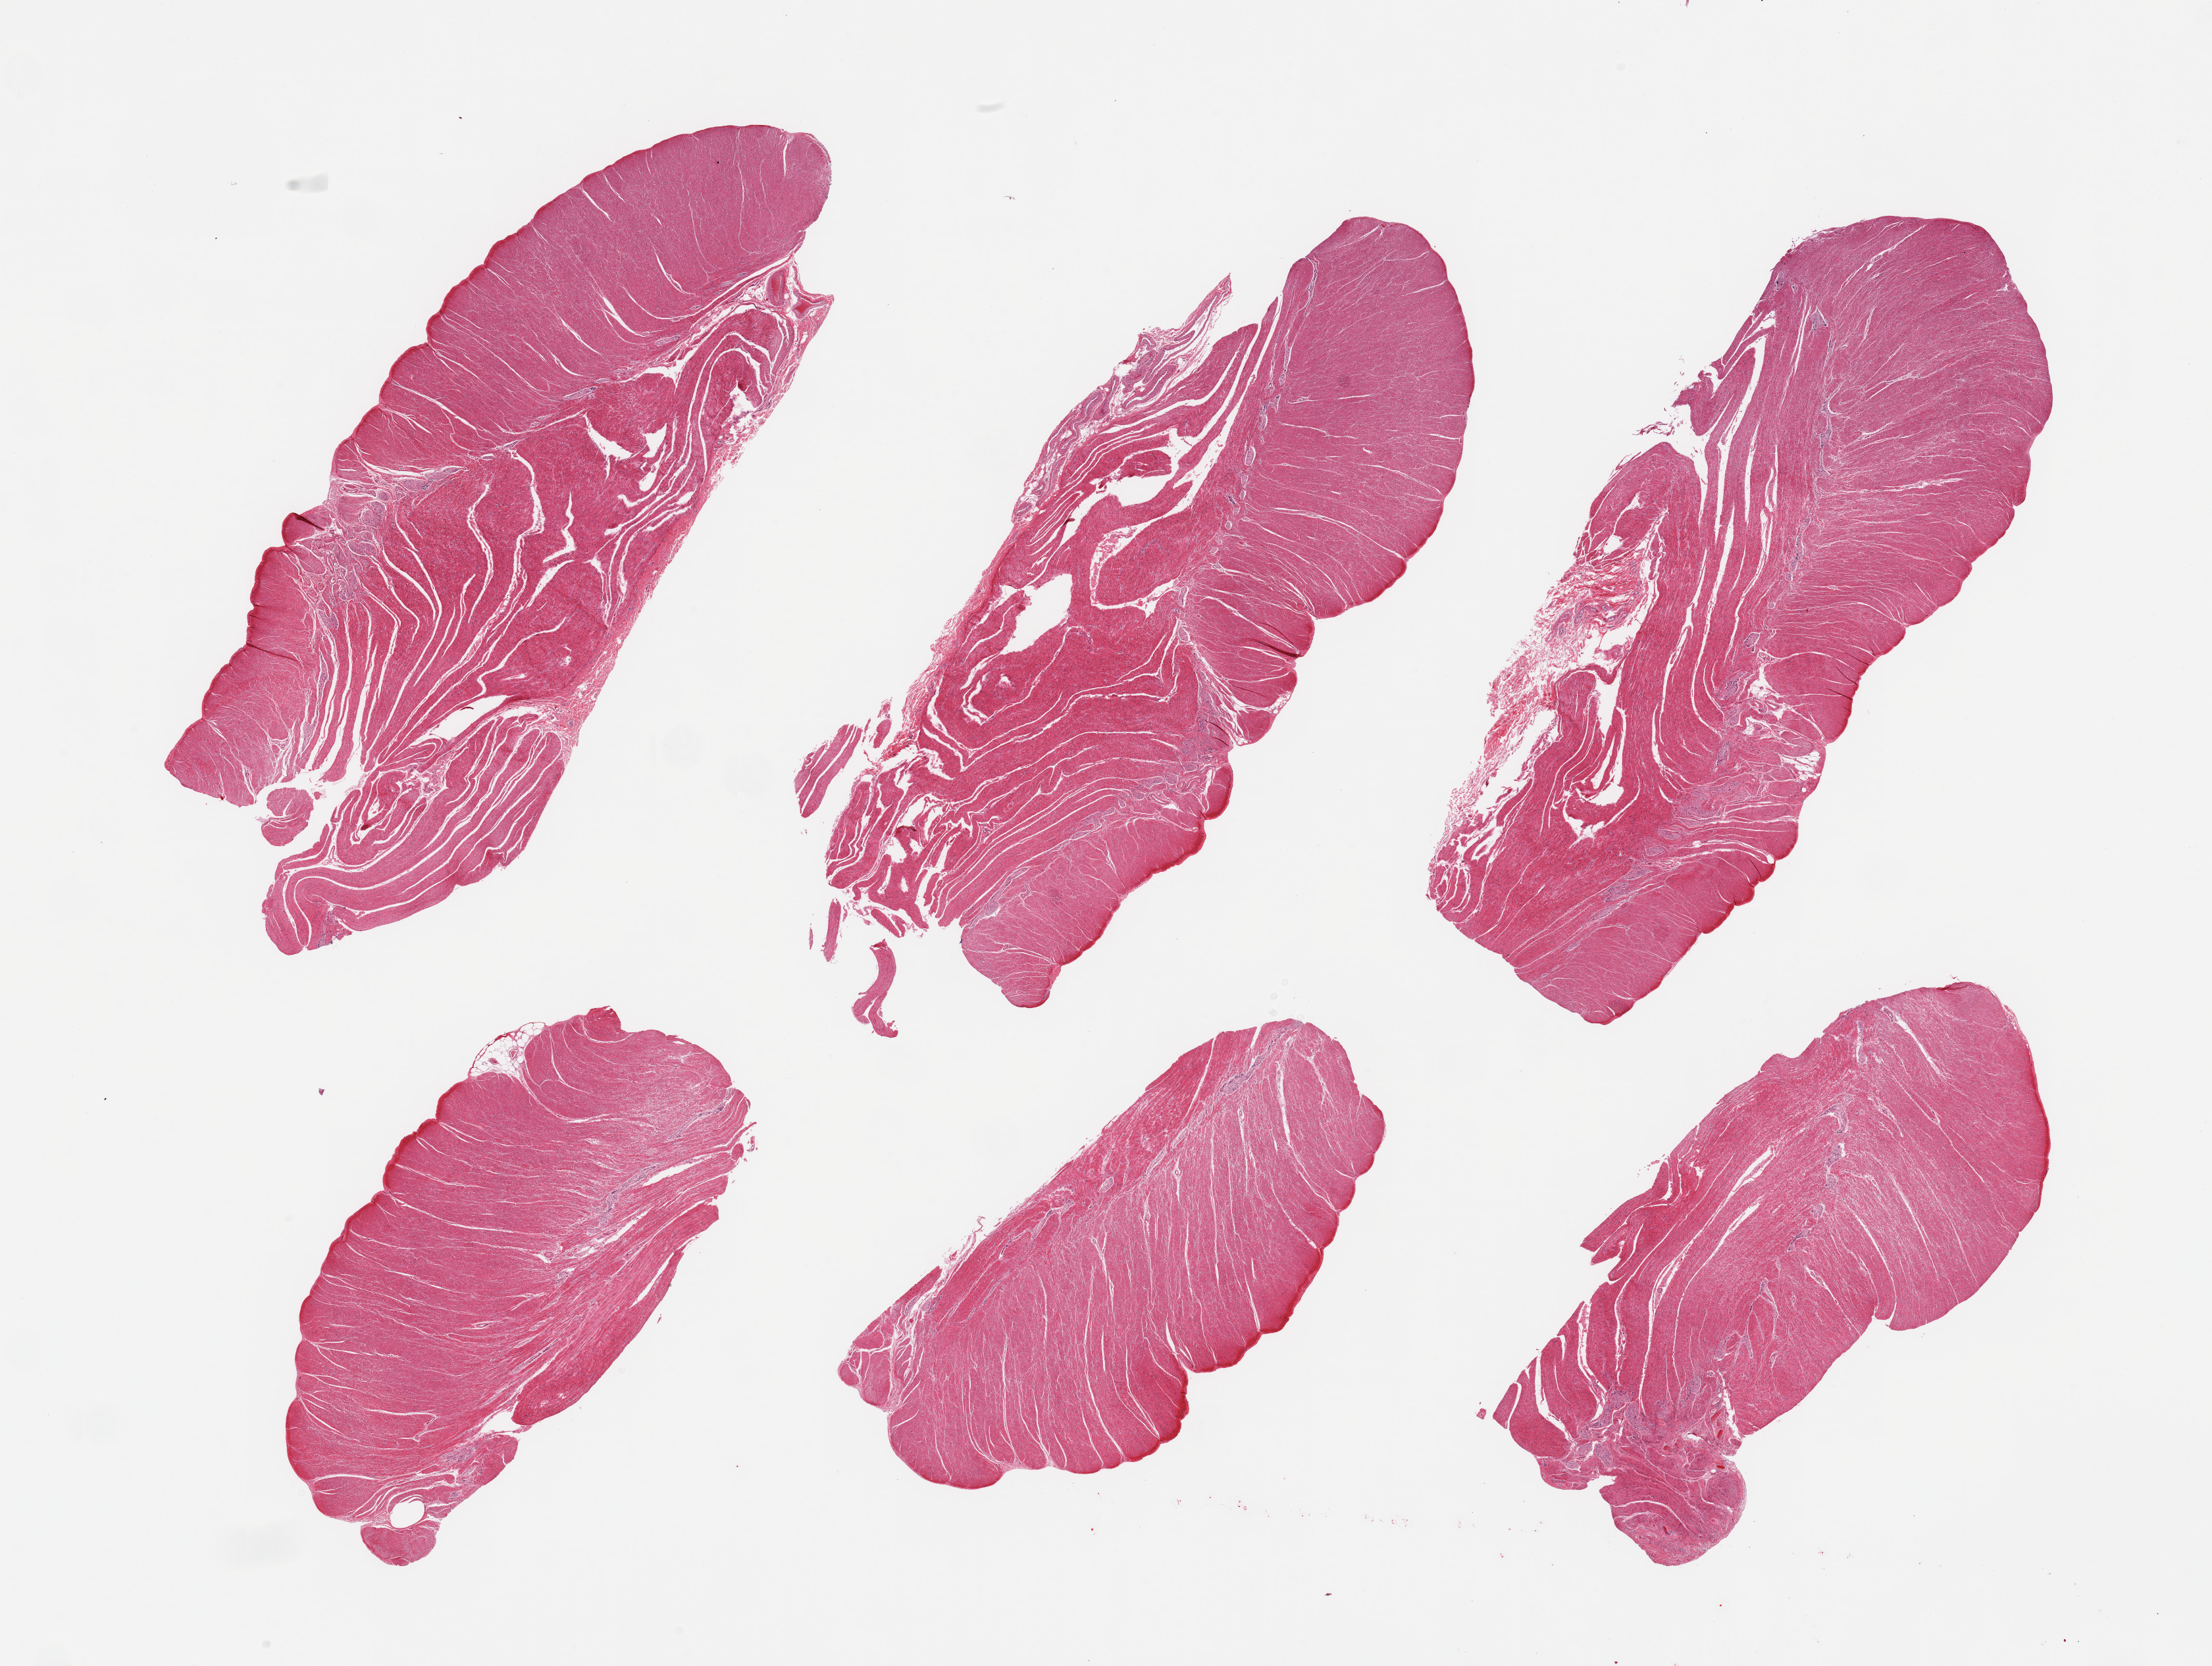
H&E whole-slide image, a low-resolution overview of the entire scanned area, about 26.6 x 20.0 mm, PAXgene-fixed paraffin-embedded (PFPE) section, section of sigmoid colon (target tissue), donor tissue sample. Male donor.
Pathologist's review note for this sample: 6 pieces; well dissected muscularis propria.